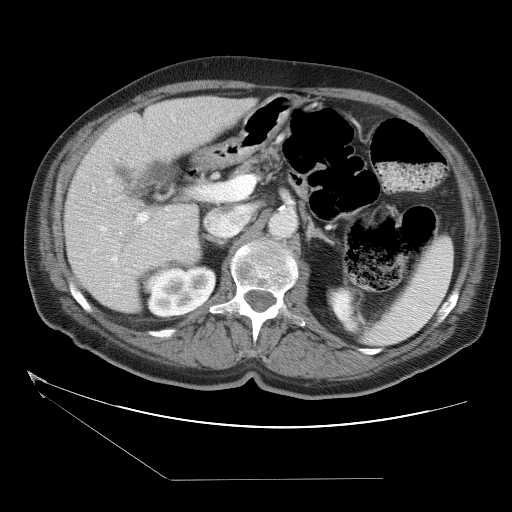
Contrast-enhanced abdominal CT (liver protocol), one axial slice; position 16 of 38 along the scan axis; reconstruction kernel STANDARD; one of 2 acquisitions stored at this slice position; soft-tissue window (W 400 / L 40 HU); 5 mm slice thickness; 512 × 512 image matrix, field of view 400 × 400 mm. From the clinical record (not read from this slice): diagnosis: hepatocellular carcinoma (patient treated with transarterial chemoembolisation; whether this scan precedes or follows treatment is not stated here); TNM stage (as recorded): Stage-II; Child-Pugh class: A.
Structures marked on this image (semi-automatically segmented with operator editing):
- liver parenchyma outside the tumour (the mass and vessels are separate outlines, so this box may not span the whole liver): bounding box (x1, y1, x2, y2) in pixels: (64, 96, 256, 312)
- mass: (175, 235, 202, 265)
- liver vessels: (83, 213, 149, 303)